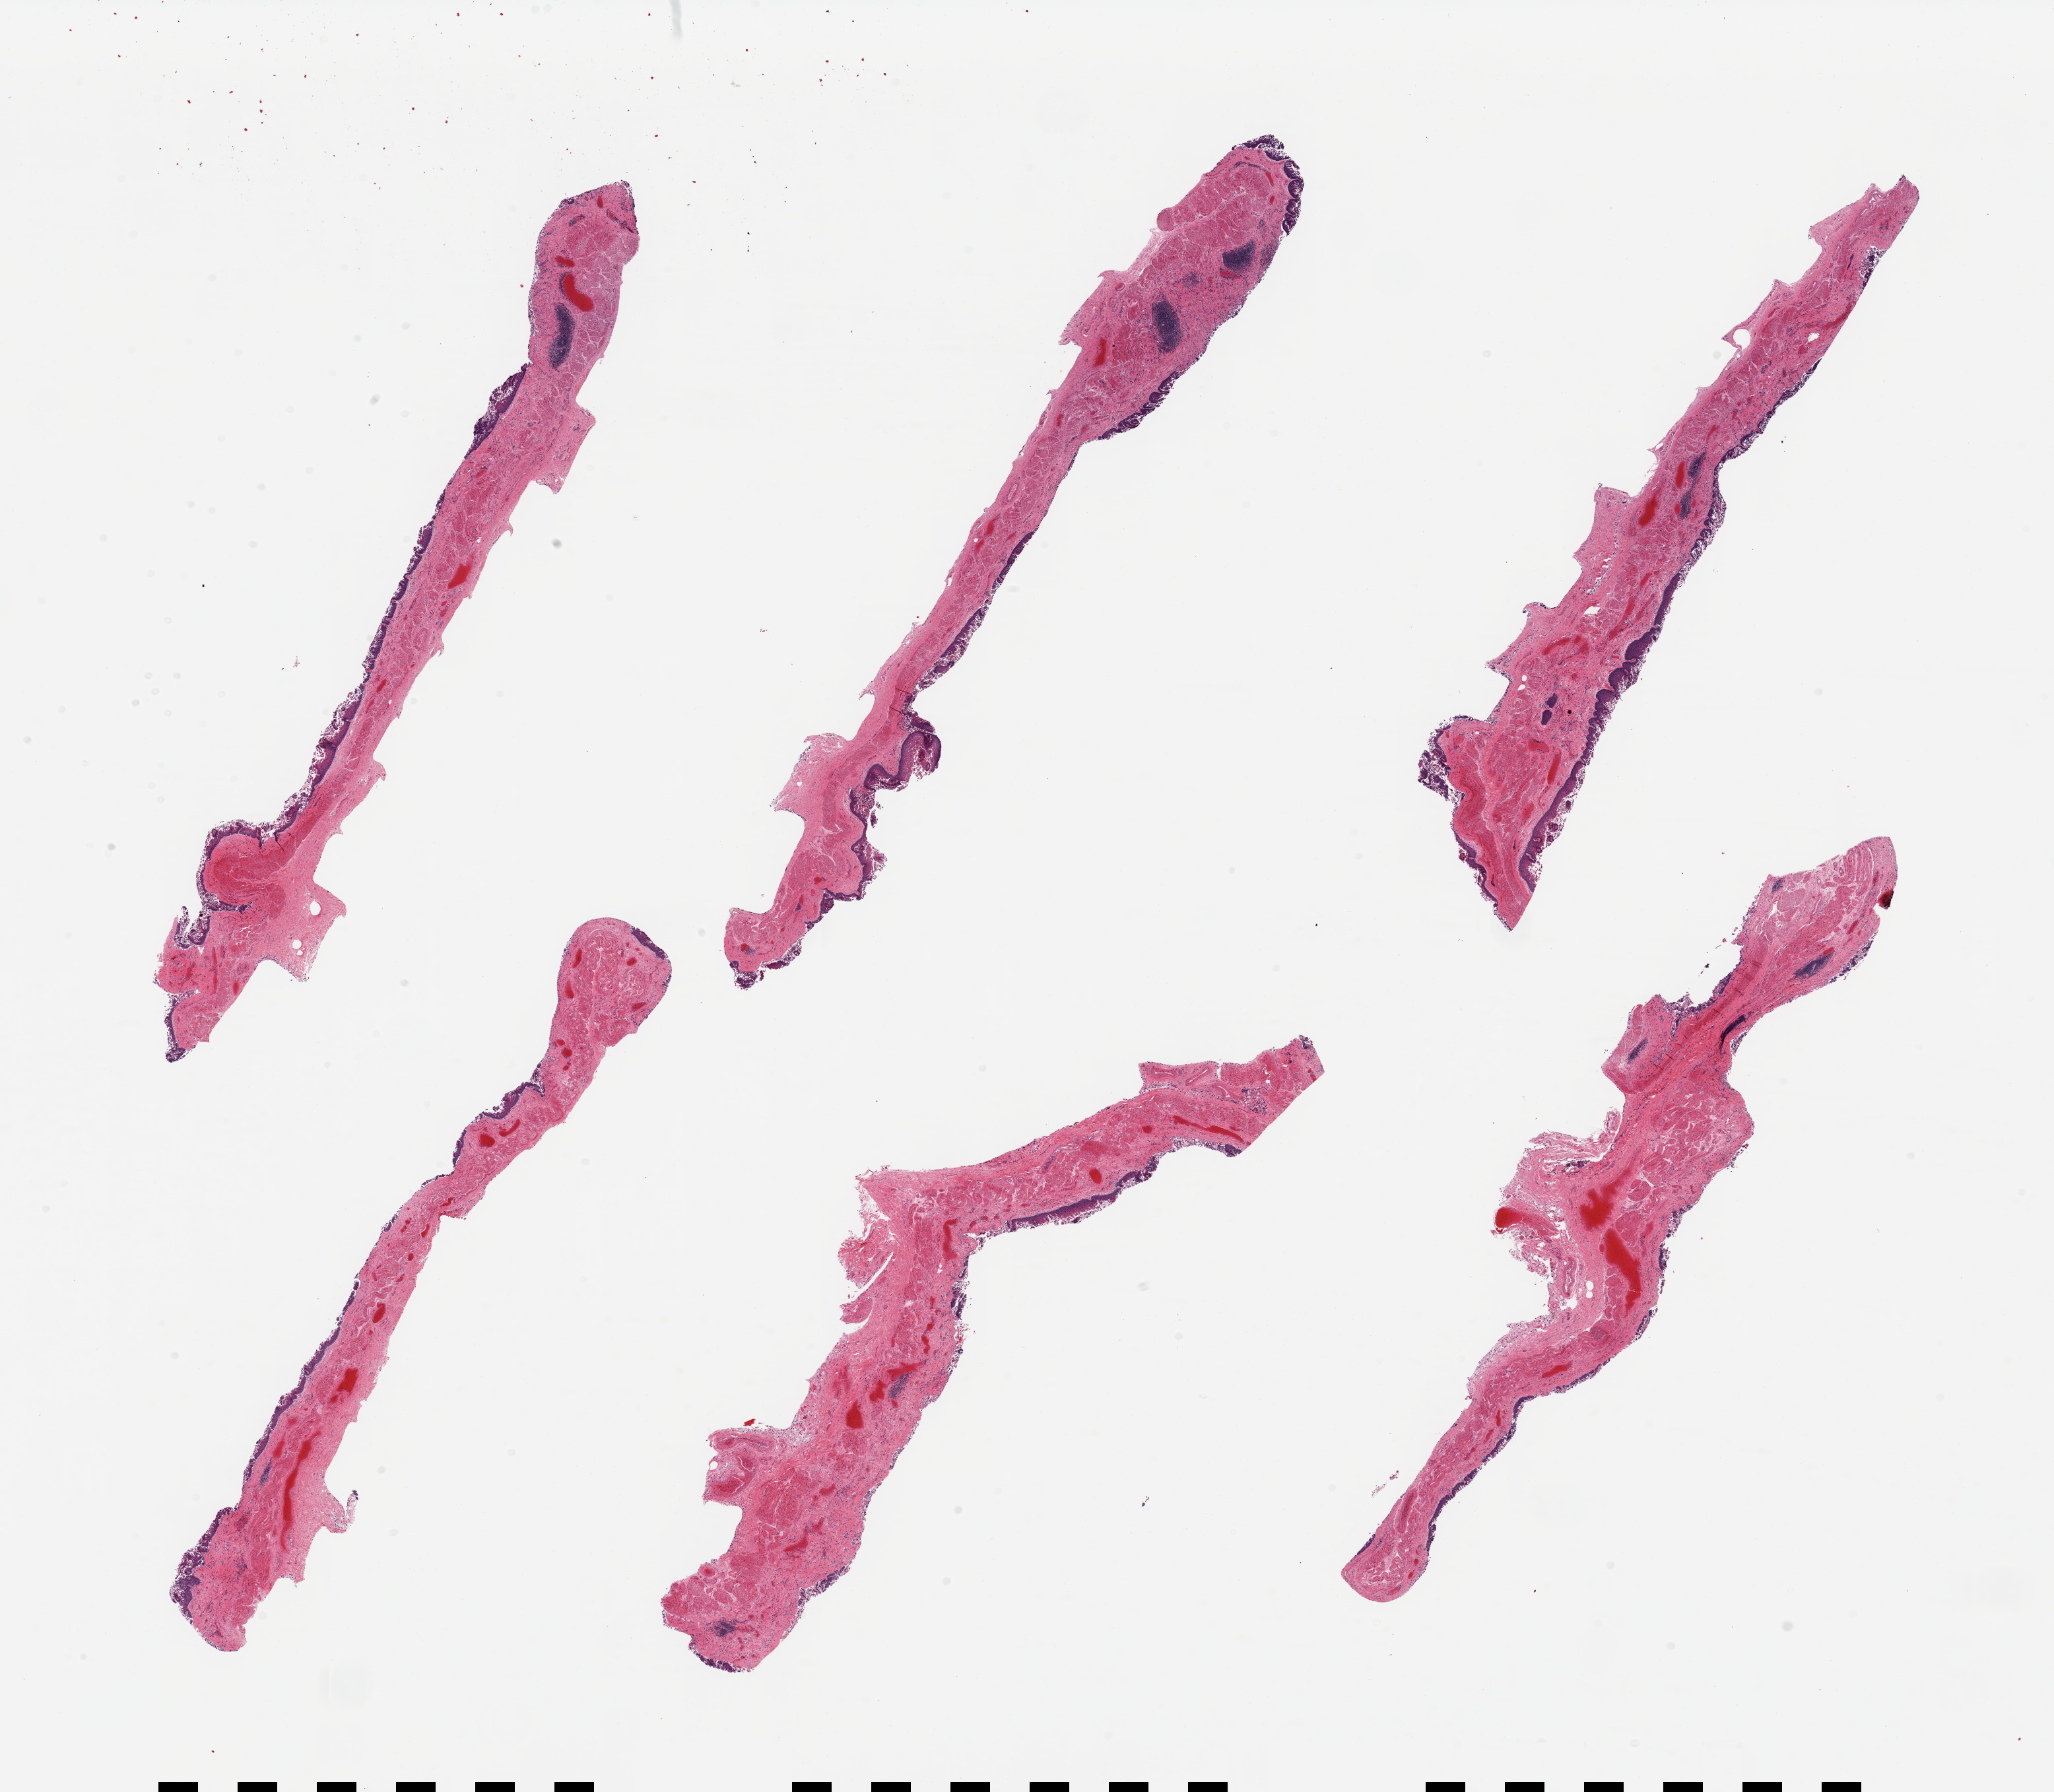
Whole-slide image, haematoxylin and eosin stain, brightfield, shown as a low-resolution overview of the whole scanned area (about 24.6 x 21.5 mm, acquisition: 20x scan). PAXgene-fixed paraffin-embedded (PFPE) section. Section of esophageal mucous membrane (target tissue). Donor tissue sample. Donor: male.
* reviewer comment on this tissue sample: 6 pieces, squamous mucosa up to ~0.2mm, ~10-15% thickness, moderate-severe sloughing